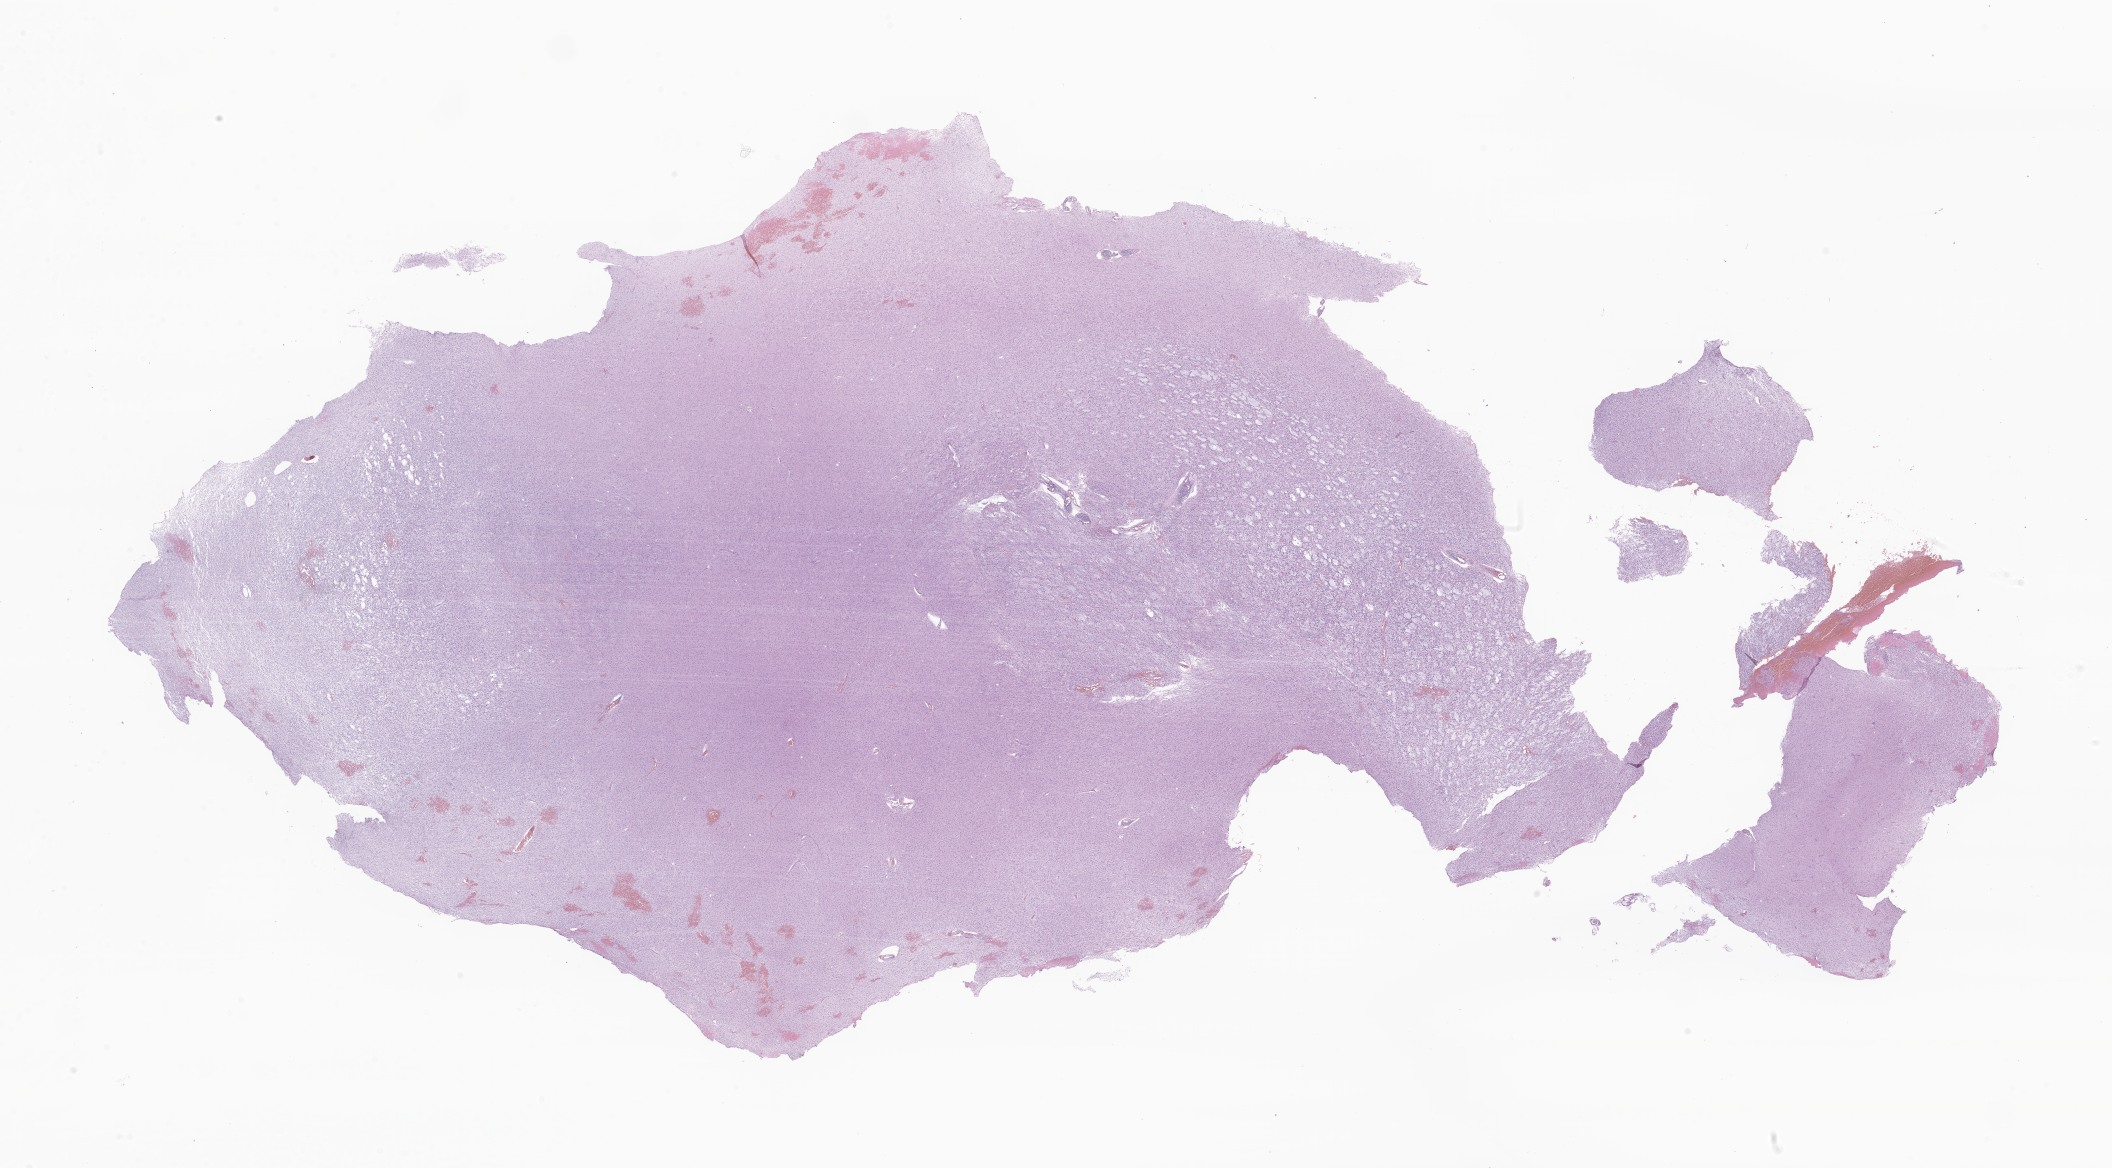
Whole-slide image, H&E stain of tumor tissue from the brain — whole scanned area (about 35.6 x 19.7 mm) shown as a low-resolution overview, formalin-fixed paraffin-embedded section. Male patient, age 282 months (23 years 6 months).
Diagnosis (ICD-O-3 morphology term): Neoplasm, uncertain whether benign or malignant.